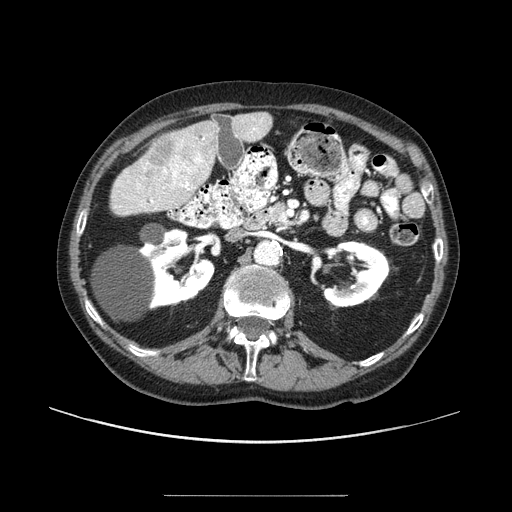
Contrast-enhanced abdominal CT (liver protocol), one axial slice. Slice 36 of 91 in the series (ordered by position). Reconstruction kernel STANDARD. 100 kVp. One of 2 acquisitions stored at this slice position. Soft-tissue window (W 400 / L 40 HU). 2.5 mm slice thickness. 512 × 512 image matrix, field of view 400 × 400 mm. From the clinical record (not read from this slice): diagnosis: hepatocellular carcinoma (patient treated with transarterial chemoembolisation; whether this scan precedes or follows treatment is not stated here); TNM stage (as recorded): Stage-I; Child-Pugh class: A; tumour differentiation: moderately differentiated; tumour nodularity: uninodular.
Structures marked on this image (semi-automatically segmented with operator editing):
- liver parenchyma outside the tumour (the mass and vessels are separate outlines, so this box may not span the whole liver): bounding box (x1, y1, x2, y2) in pixels: (174, 112, 272, 204)
- mass: (139, 132, 213, 187)
- liver vessels: (185, 119, 262, 190)